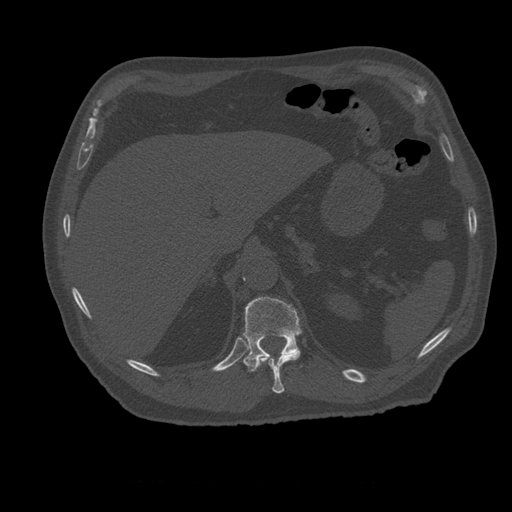
CT including the spine, one axial slice; reconstruction kernel STANDARD; 120 kVp; bone window (W 1800 / L 400 HU); 1.25 mm slice thickness; 512 × 512 image matrix, field of view 407 × 407 mm. Patient age 73 years. Case-level facts recorded for this patient, not image findings: primary cancer: prostate.
Outlined on this slice (semi-automatically segmented with operator editing):
- T11 vertebra: bounding box [x1, y1, x2, y2] px = [259, 352, 301, 394]
- T12 vertebra: [243, 297, 302, 372]